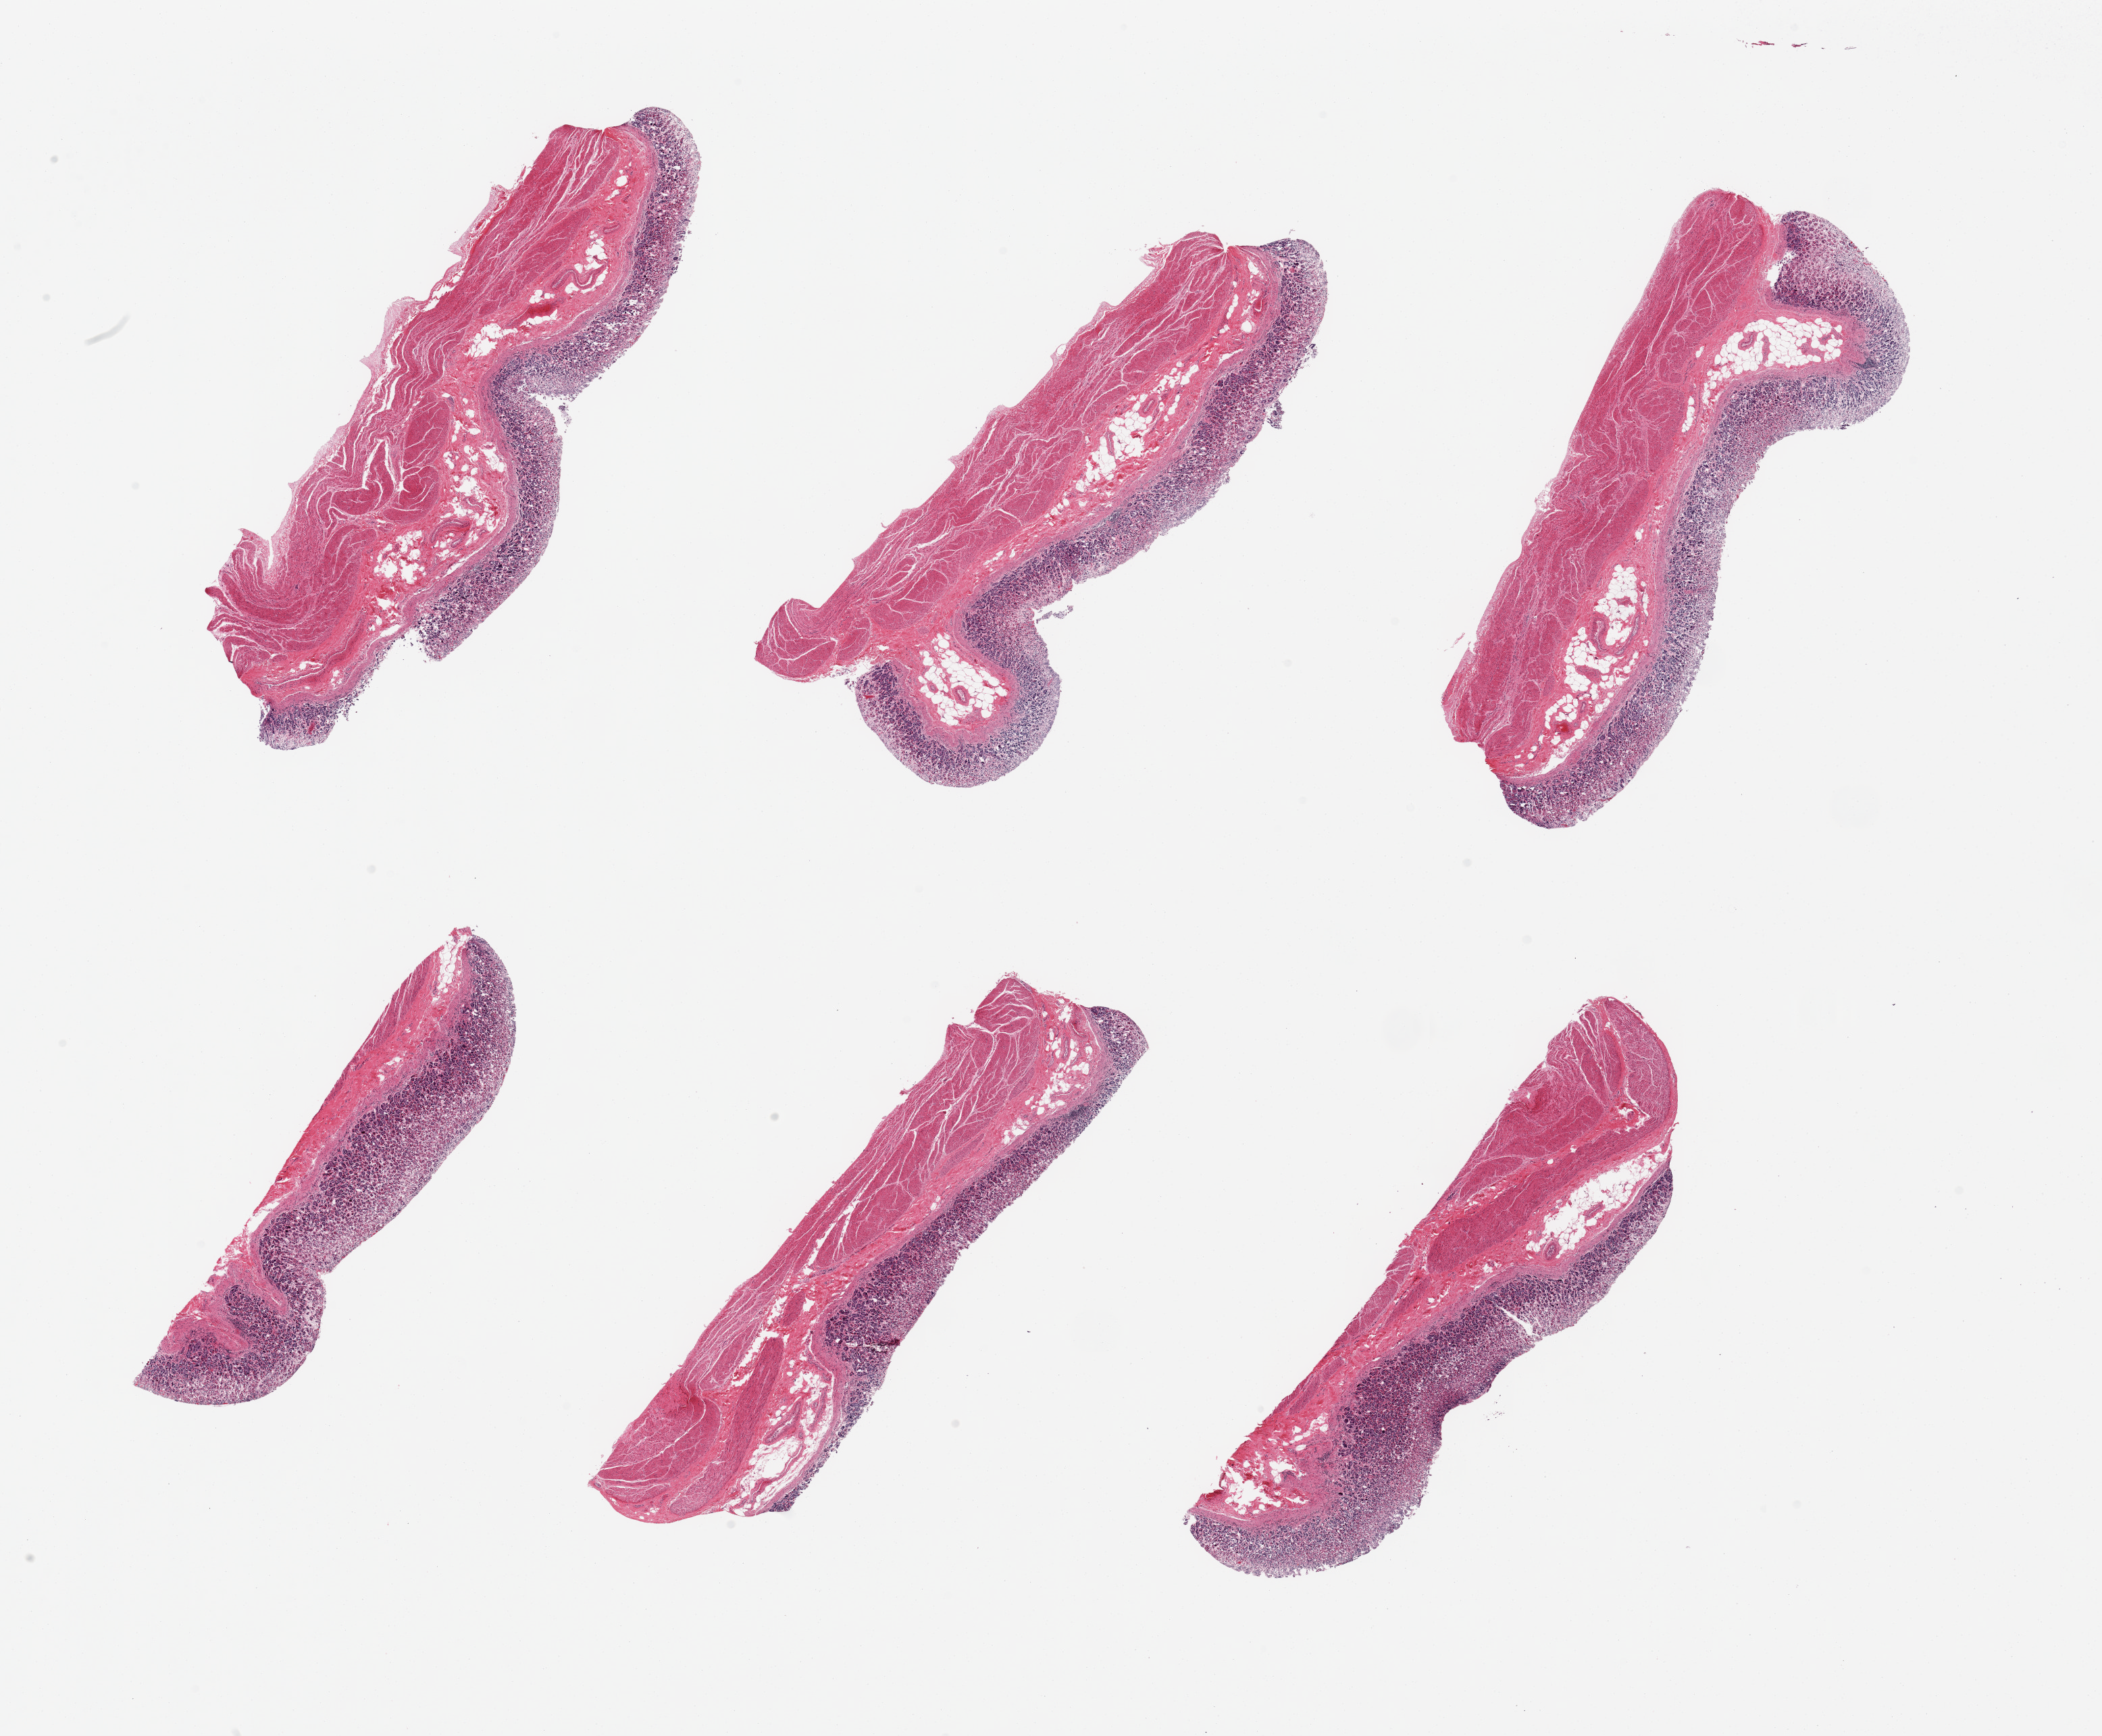
Digitized H&E-stained section — whole scanned area (about 24.6 x 20.3 mm, from a 20x scan) shown as a low-resolution overview, PAXgene-fixed, paraffin-embedded tissue, target tissue: stomach, donor tissue sample. Donor: male.
Pathologist's review note for this sample: 6 pieces; superficial glands more autolyzed than deeper.